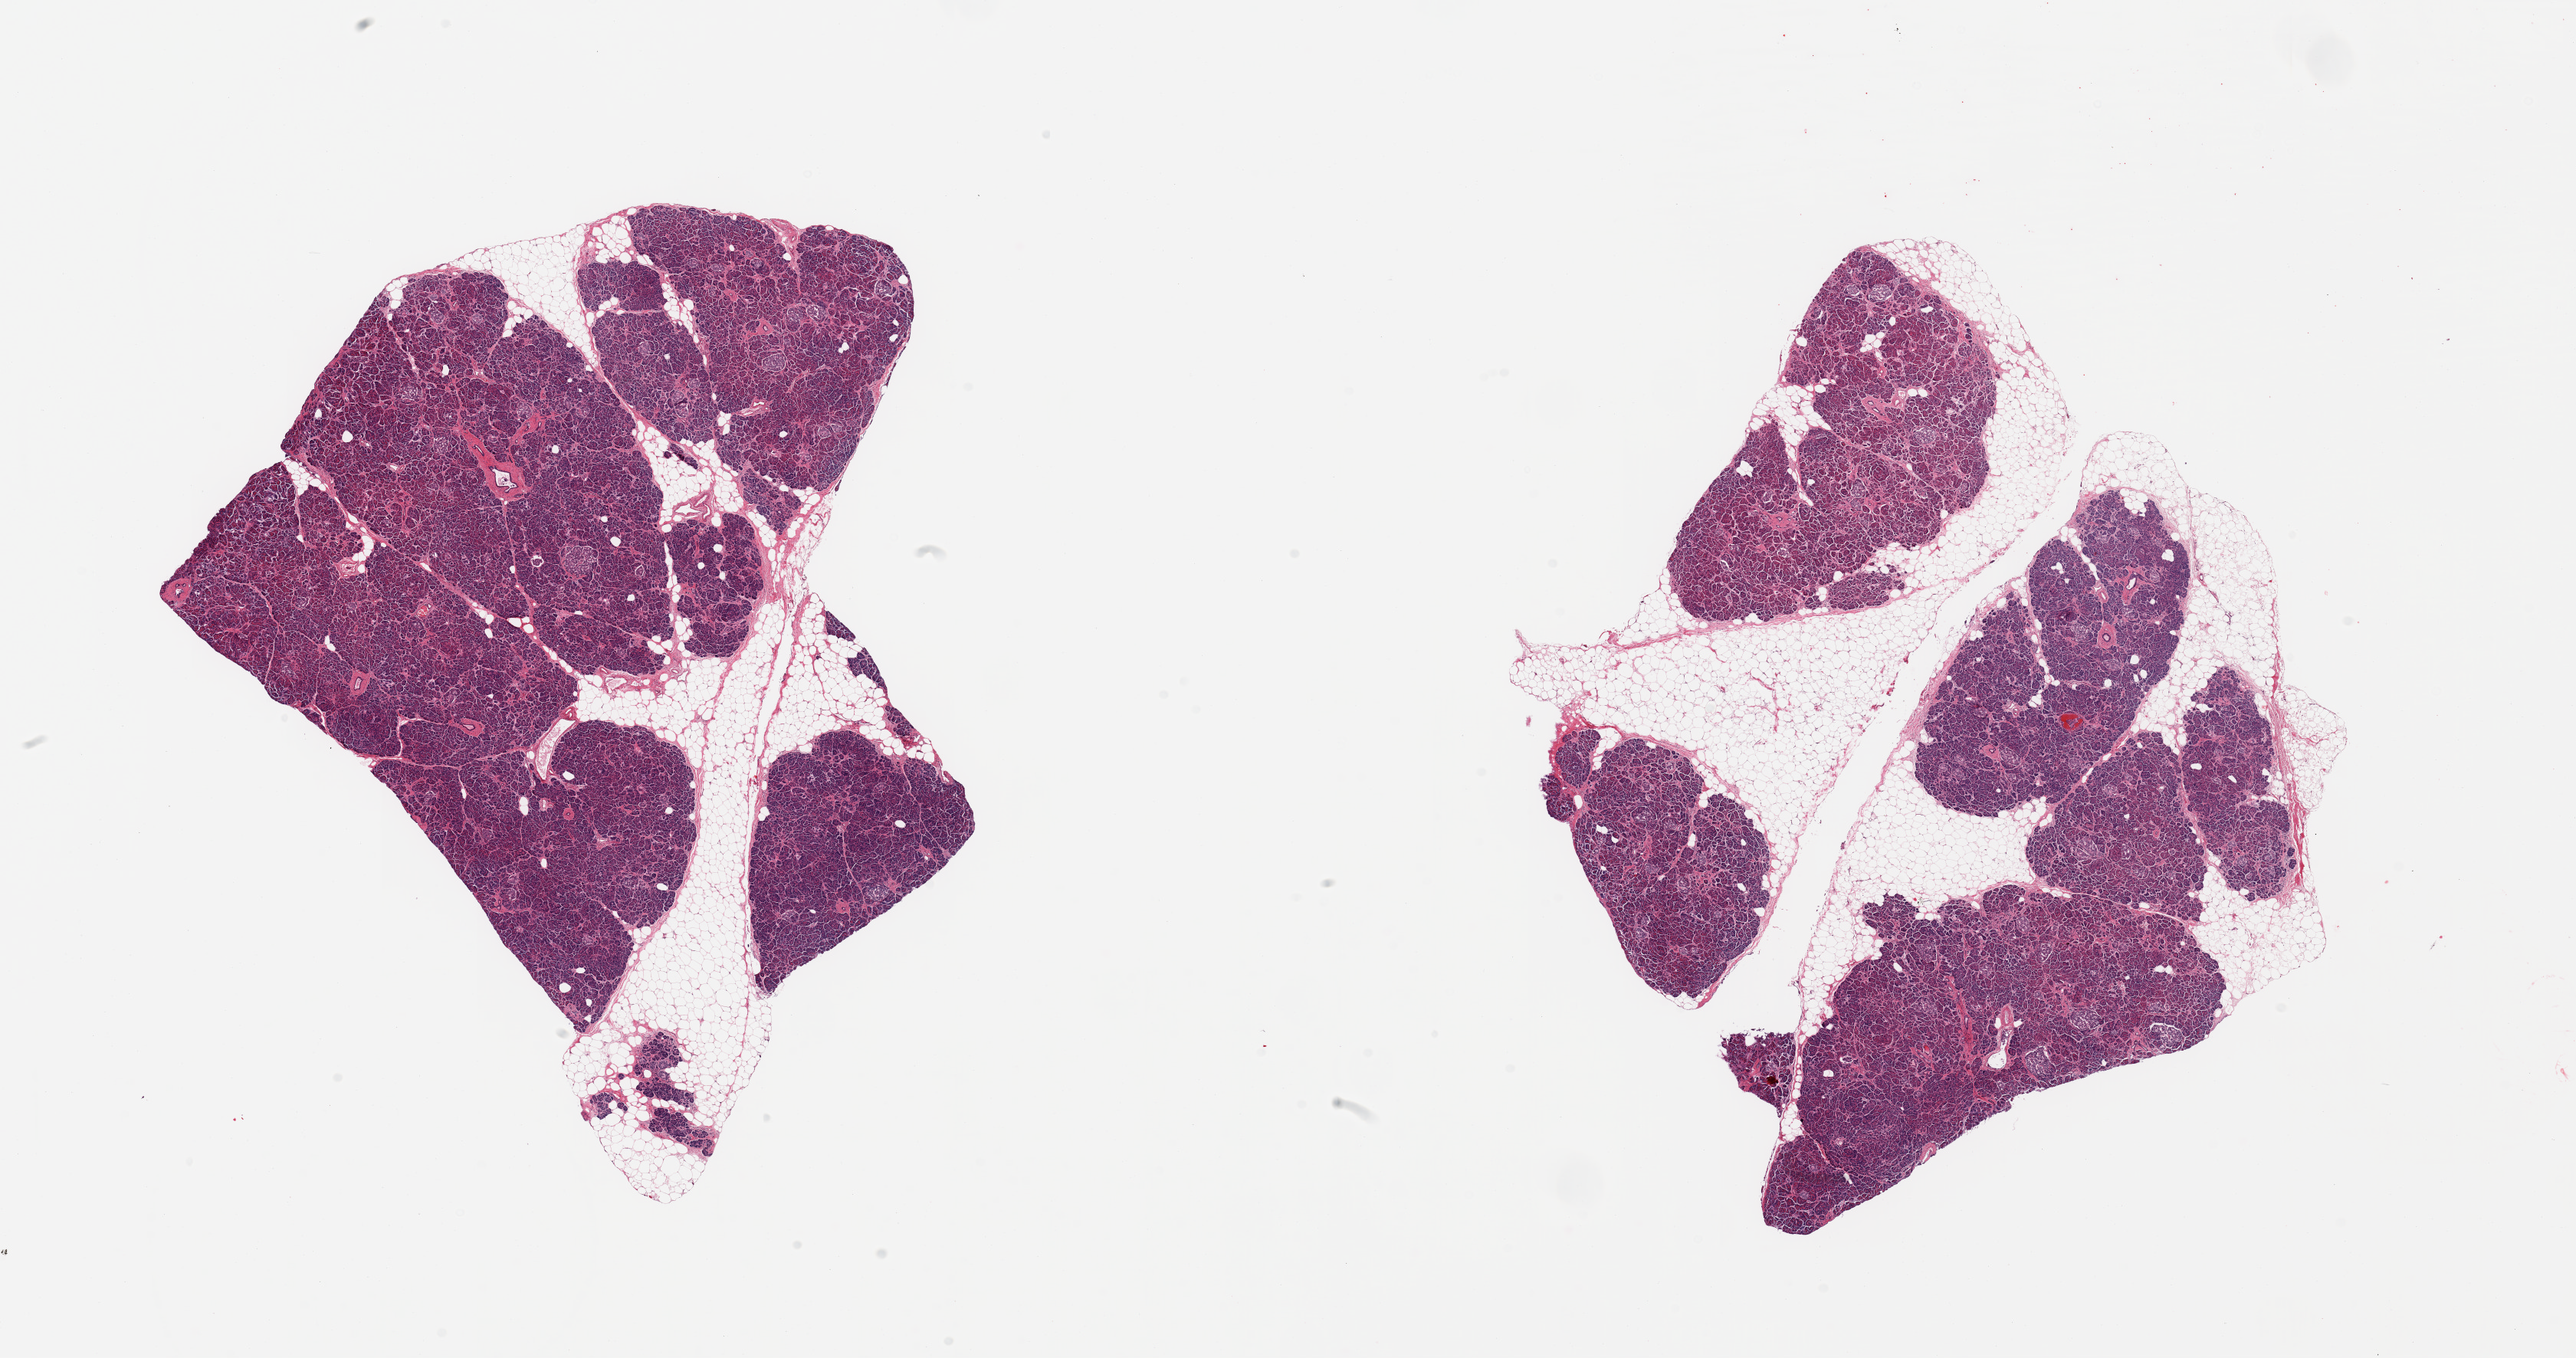
H&E whole-slide image, brightfield — shown as a low-resolution overview of the whole scanned area (about 26.6 x 14.0 mm), PAXgene-fixed, paraffin-embedded tissue, section of pancreas (target tissue), donor tissue sample. Donor sex: male.
Reviewer comment on this tissue sample: 2 pieces; 40 & 20% internal fat.